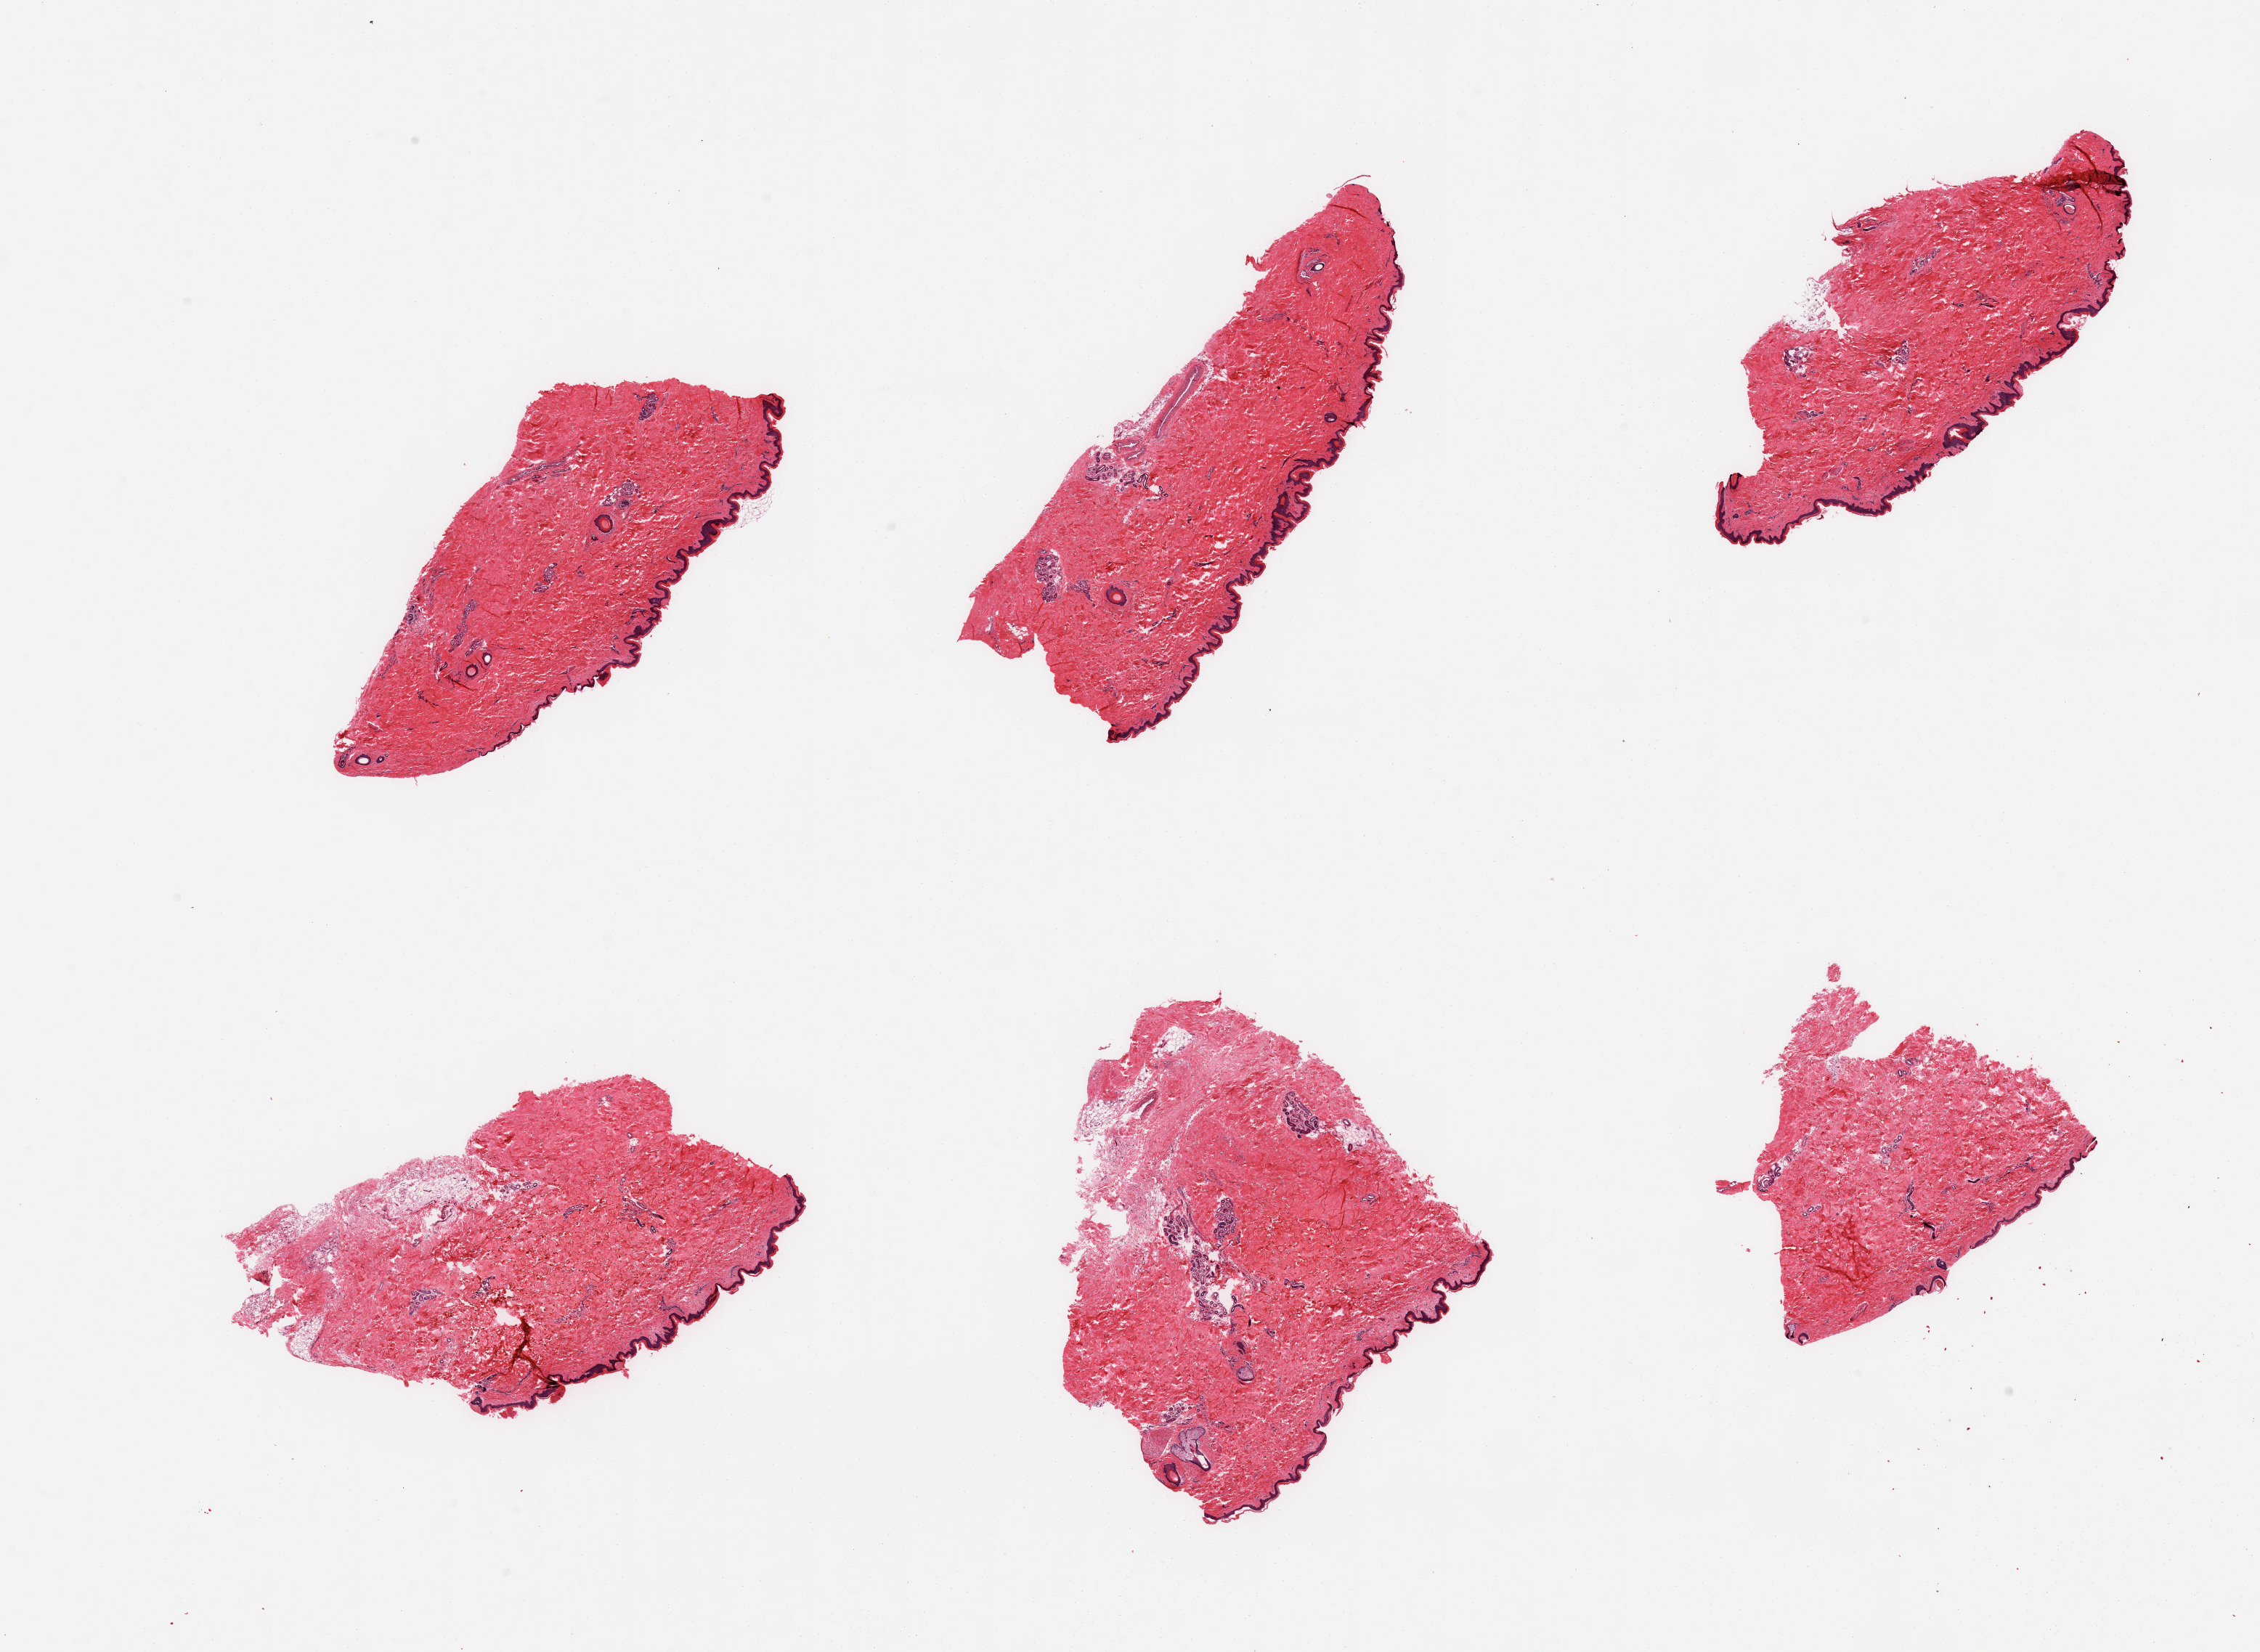
Digitized haematoxylin and eosin-stained section, low-resolution overview of the scanned area, about 24.6 x 18.0 mm; PAXgene-fixed paraffin-embedded (PFPE) section; sampled site (target tissue): skin of lower leg; donor tissue sample. Male donor.
* review note (as recorded): 6 pieces, no significant dermal fat, squamous epithelium is ~25-35 microns